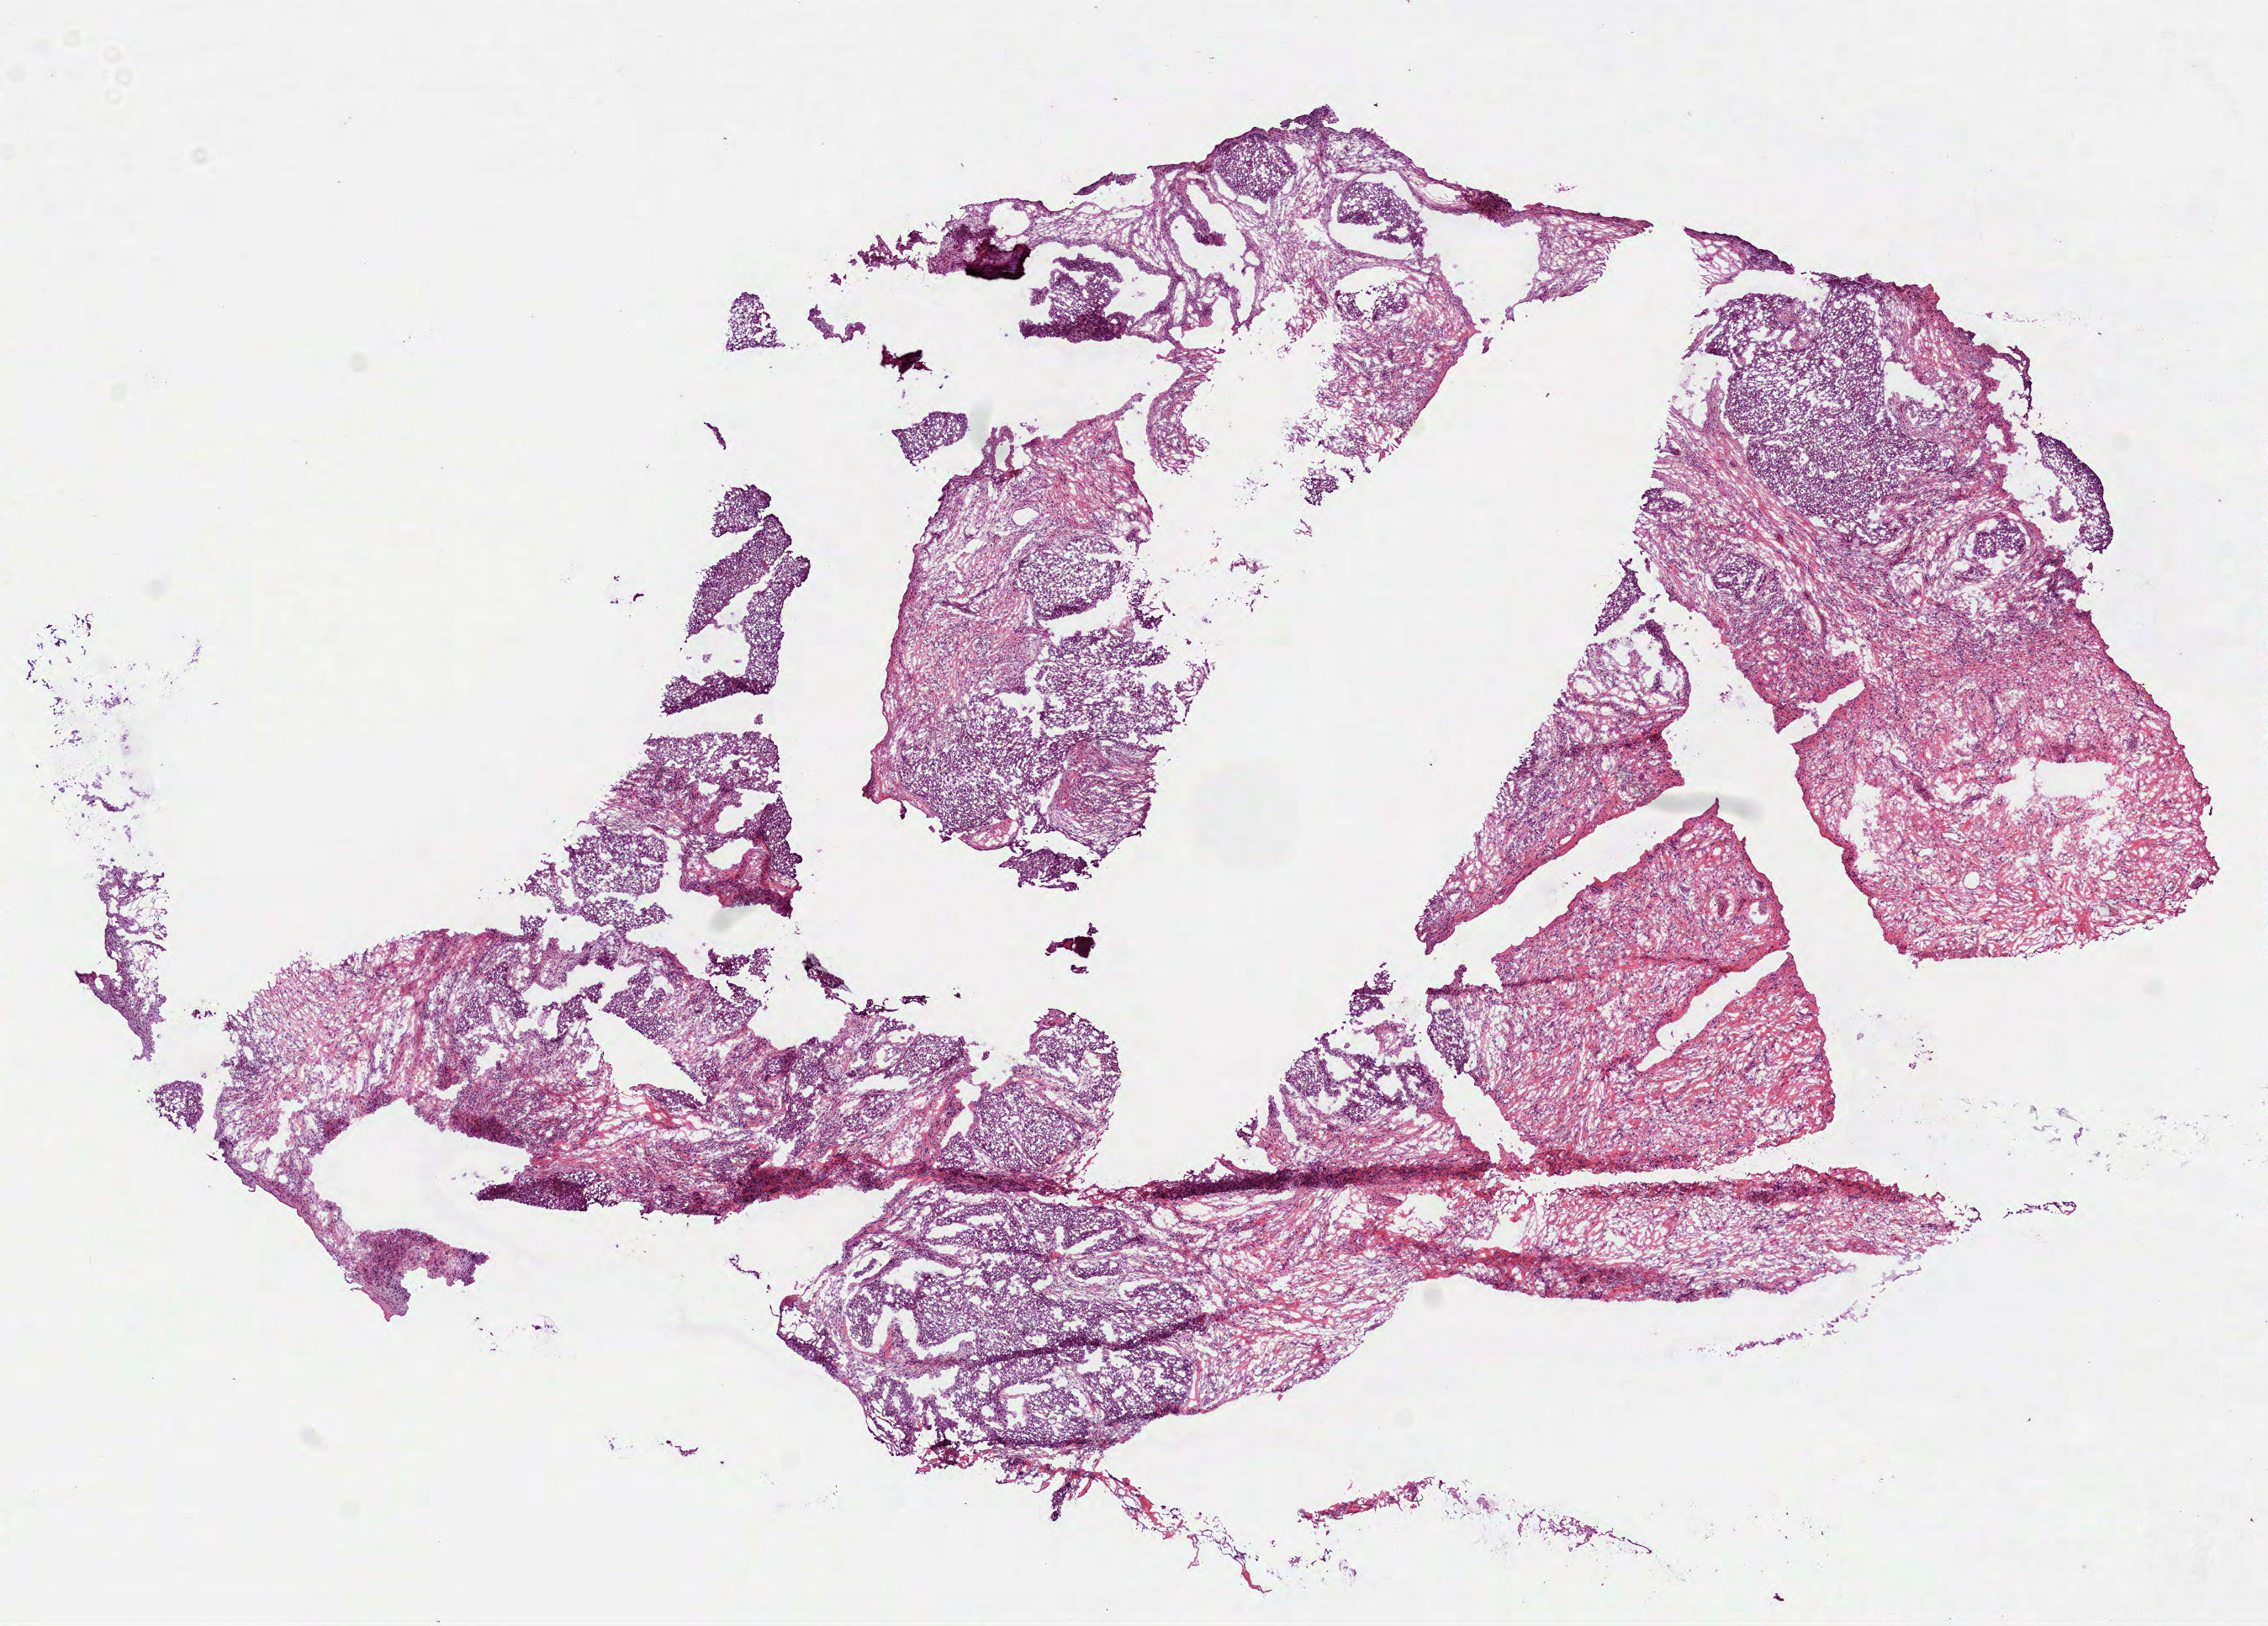
H&E-stained whole-slide image, a low-resolution overview of the entire scanned area, about 10.9 x 7.8 mm; frozen section from the bottom of the tissue portion; primary tumour sample from the head and neck. Patient: male, age at initial diagnosis 67 years. Histologic grade: G3 (poorly differentiated). Slide review estimates, as recorded: tumour cells 60%, tumour nuclei 65%, normal cells 0%, stromal cells 40%, necrosis 0%.
* pathologic diagnosis: Squamous cell carcinoma, NOS (floor of mouth, NOS)
* AJCC pathologic stage: II